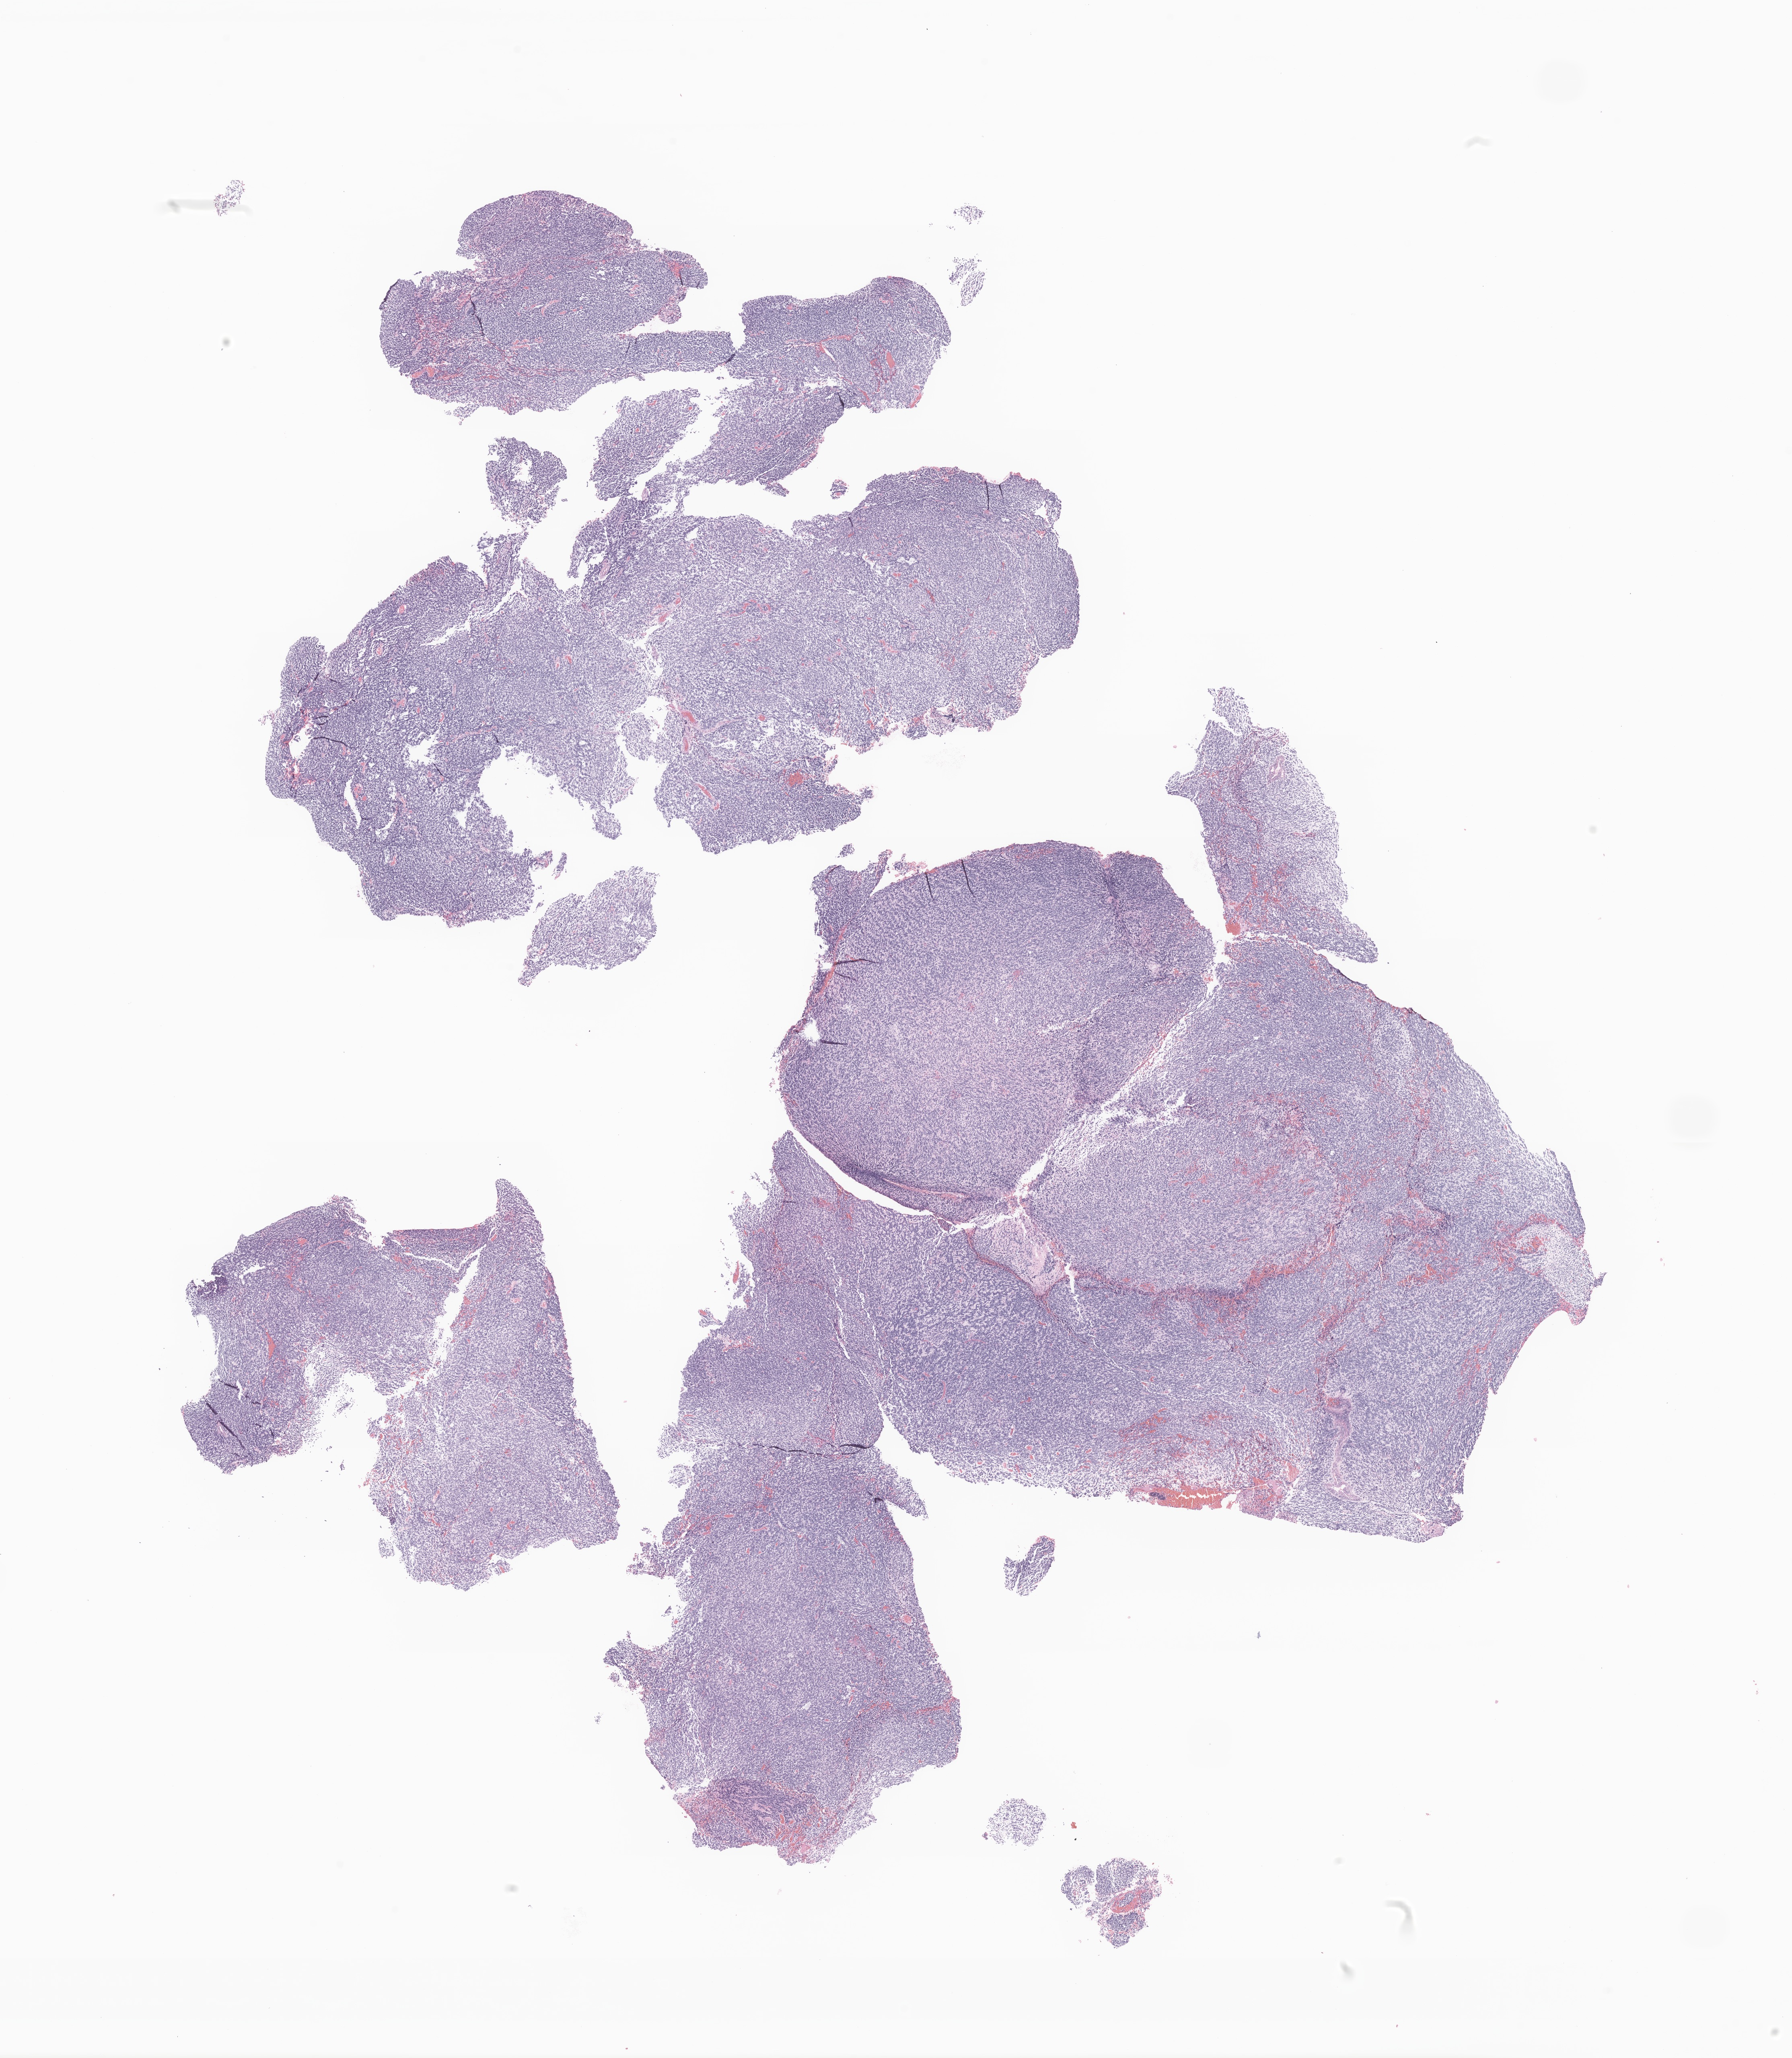
Digitized H&E-stained section of tumor tissue from the cerebral ventricle, low-resolution overview of the scanned area, about 18.8 x 21.6 mm. Formalin-fixed paraffin-embedded section. Patient: male, age 110 months.
* diagnosis: Medulloblastoma, NOS